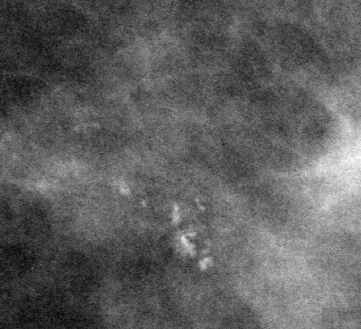
Crop from a digitized film mammogram around one marked abnormality; left breast; CC view; BI-RADS breast density category 3 (scale 1–4).
Calcifications, morphology amorphous, distribution clustered; BI-RADS assessment category 4; subtlety rating 3 on a 1 (subtle) to 5 (obvious) scale; pathology result (as recorded, not read from the image): benign.